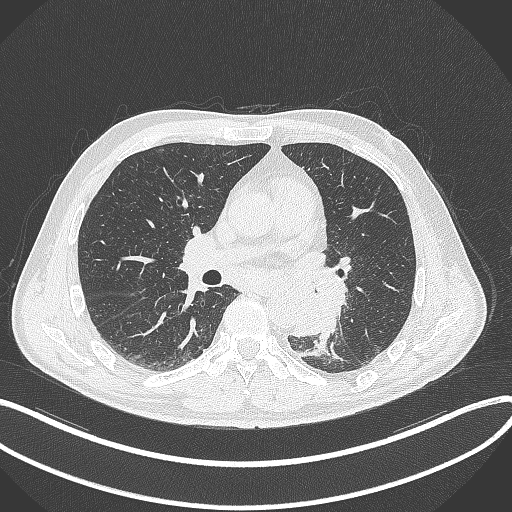
Chest CT, one axial slice. Slice 178 of 329 in the series (ordered by position). Reconstruction kernel B70f. 120 kVp. Lung window (W 1500 / L -600 HU). 1 mm slice thickness. 512 × 512 image matrix. Patient: male, 59 years. From the clinical record (not read from this slice): clinical TNM (as recorded): T2a N2 M0.
Annotated regions visible in this slice (rectangle marked by the reading radiologist):
- lung tumour (recorded histology: squamous cell carcinoma): bounding box (x1, y1, x2, y2) in pixels: (281, 268, 346, 338)